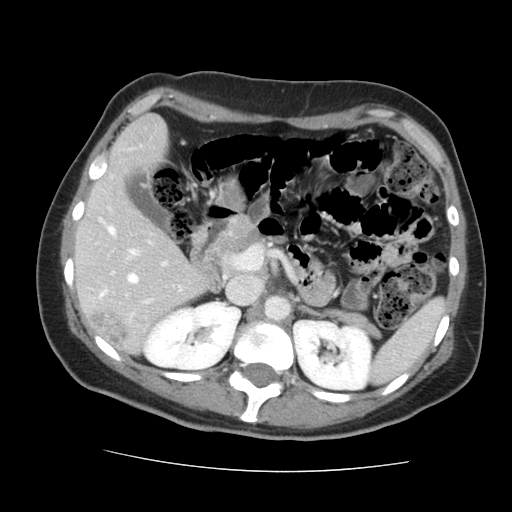
Contrast-enhanced abdominal CT, one axial slice. Slice 84 of 144 in the series (ordered by position). 120 kVp. Intravenous contrast given. Soft-tissue window (W 400 / L 40 HU). 2.5 mm slice thickness. 512 × 512 image matrix. Female patient, age 46 years. Case-level facts recorded for this patient, not image findings: diagnosis: colorectal cancer liver metastases, imaged before liver resection; multiple liver metastases: no; largest metastasis: 2.8 cm; disease in both lobes: no.
Outlined on this slice (manually delineated by an expert):
- hepatic veins: bounding box [x1, y1, x2, y2] px = [102, 274, 138, 296]
- liver: [77, 117, 206, 350]
- planned liver remnant (the part of the liver to remain after resection): [77, 117, 206, 344]
- portal vein (with intrahepatic branches): [109, 228, 167, 304]
- liver metastasis: [91, 311, 128, 346]